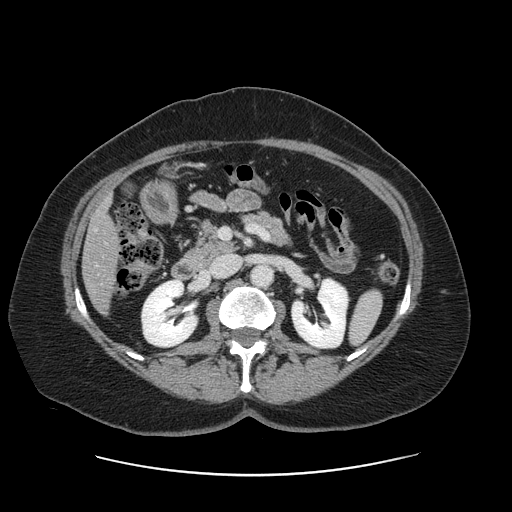
Contrast-enhanced abdominal CT, one axial slice; position 57 of 161 along the scan axis; intravenous contrast given; soft-tissue window (W 400 / L 40 HU); 2.5 mm slice thickness; 512 × 512 image matrix, field of view 398 × 398 mm. Female patient, age 62 years. From the clinical record (not read from this slice): diagnosis: colorectal cancer liver metastases, imaged before liver resection; multiple liver metastases: no; largest metastasis: 2.5 cm.
Annotated regions visible in this slice (expert manual segmentation):
- liver: bounding box (x1, y1, x2, y2) in pixels: (84, 202, 118, 311)